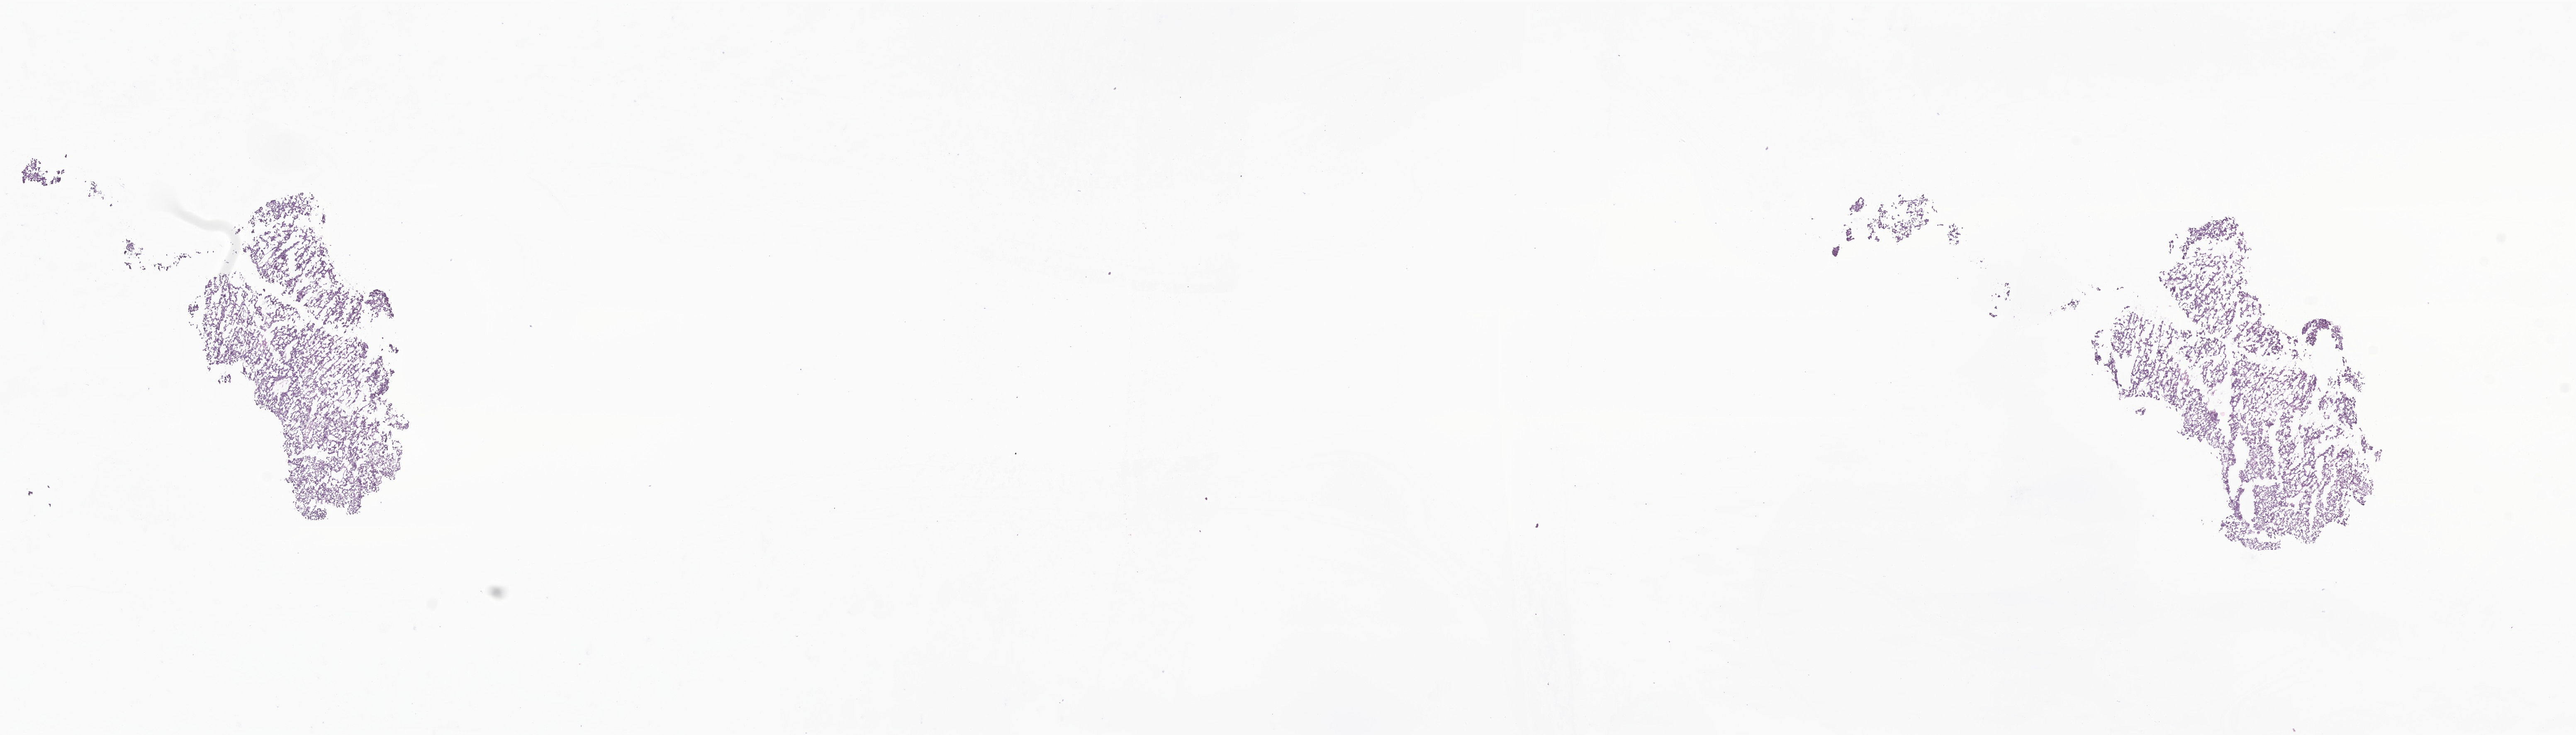
Digitized H&E-stained section of tumor tissue from the tail of pancreas, a low-resolution overview of the entire scanned area, about 26.2 x 7.5 mm; frozen section (OCT-embedded). Patient: female, age 74 months.
Recorded diagnosis: Pancreatoblastoma.